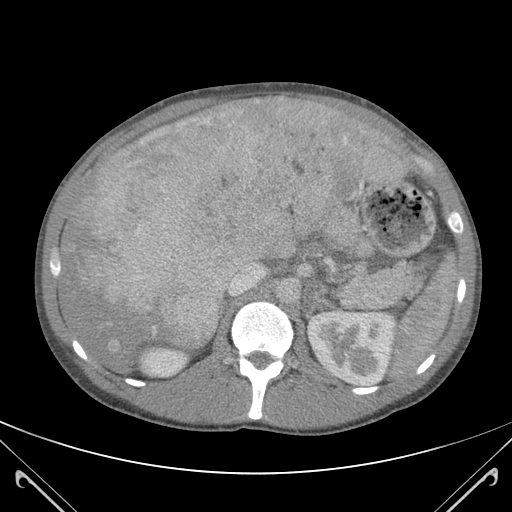
Contrast-enhanced abdominal CT (liver protocol), one axial slice. Position 72 of 118 along the scan axis. 120 kVp. Soft-tissue window (W 400 / L 40 HU). 512 × 512 image matrix, field of view 380 × 380 mm. Case-level facts recorded for this patient, not image findings: diagnosis: hepatocellular carcinoma (patient treated with transarterial chemoembolisation; whether this scan precedes or follows treatment is not stated here); TNM stage (as recorded): Stage-IIIB; Child-Pugh class: A; tumour nodularity: uninodular.
Outlined on this slice (semi-automatically segmented with operator editing):
- abdominal aorta: box from (x=276, y=278) to (x=299, y=303) px
- liver parenchyma outside the tumour (the mass and vessels are separate outlines, so this box may not span the whole liver): (x=59, y=98)–(x=406, y=370)
- mass: (x=65, y=99)–(x=394, y=346)
- liver vessels: (x=59, y=99)–(x=362, y=296)